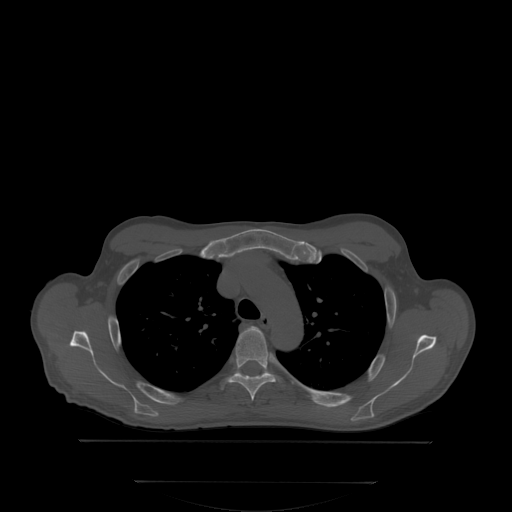
CT including the spine, one axial slice. Slice 258 of 350 in the series (ordered by position). Bone window (W 1800 / L 400 HU). 2.5 mm slice thickness. 512 × 512 image matrix, field of view 500 × 500 mm. Male patient, age 58 years. From the clinical record (not read from this slice): primary cancer: prostate.
Annotated regions visible in this slice (semi-automatic segmentation, software-assisted and operator-edited):
- T4 vertebra: bounding box [x1, y1, x2, y2] px = [220, 329, 277, 400]